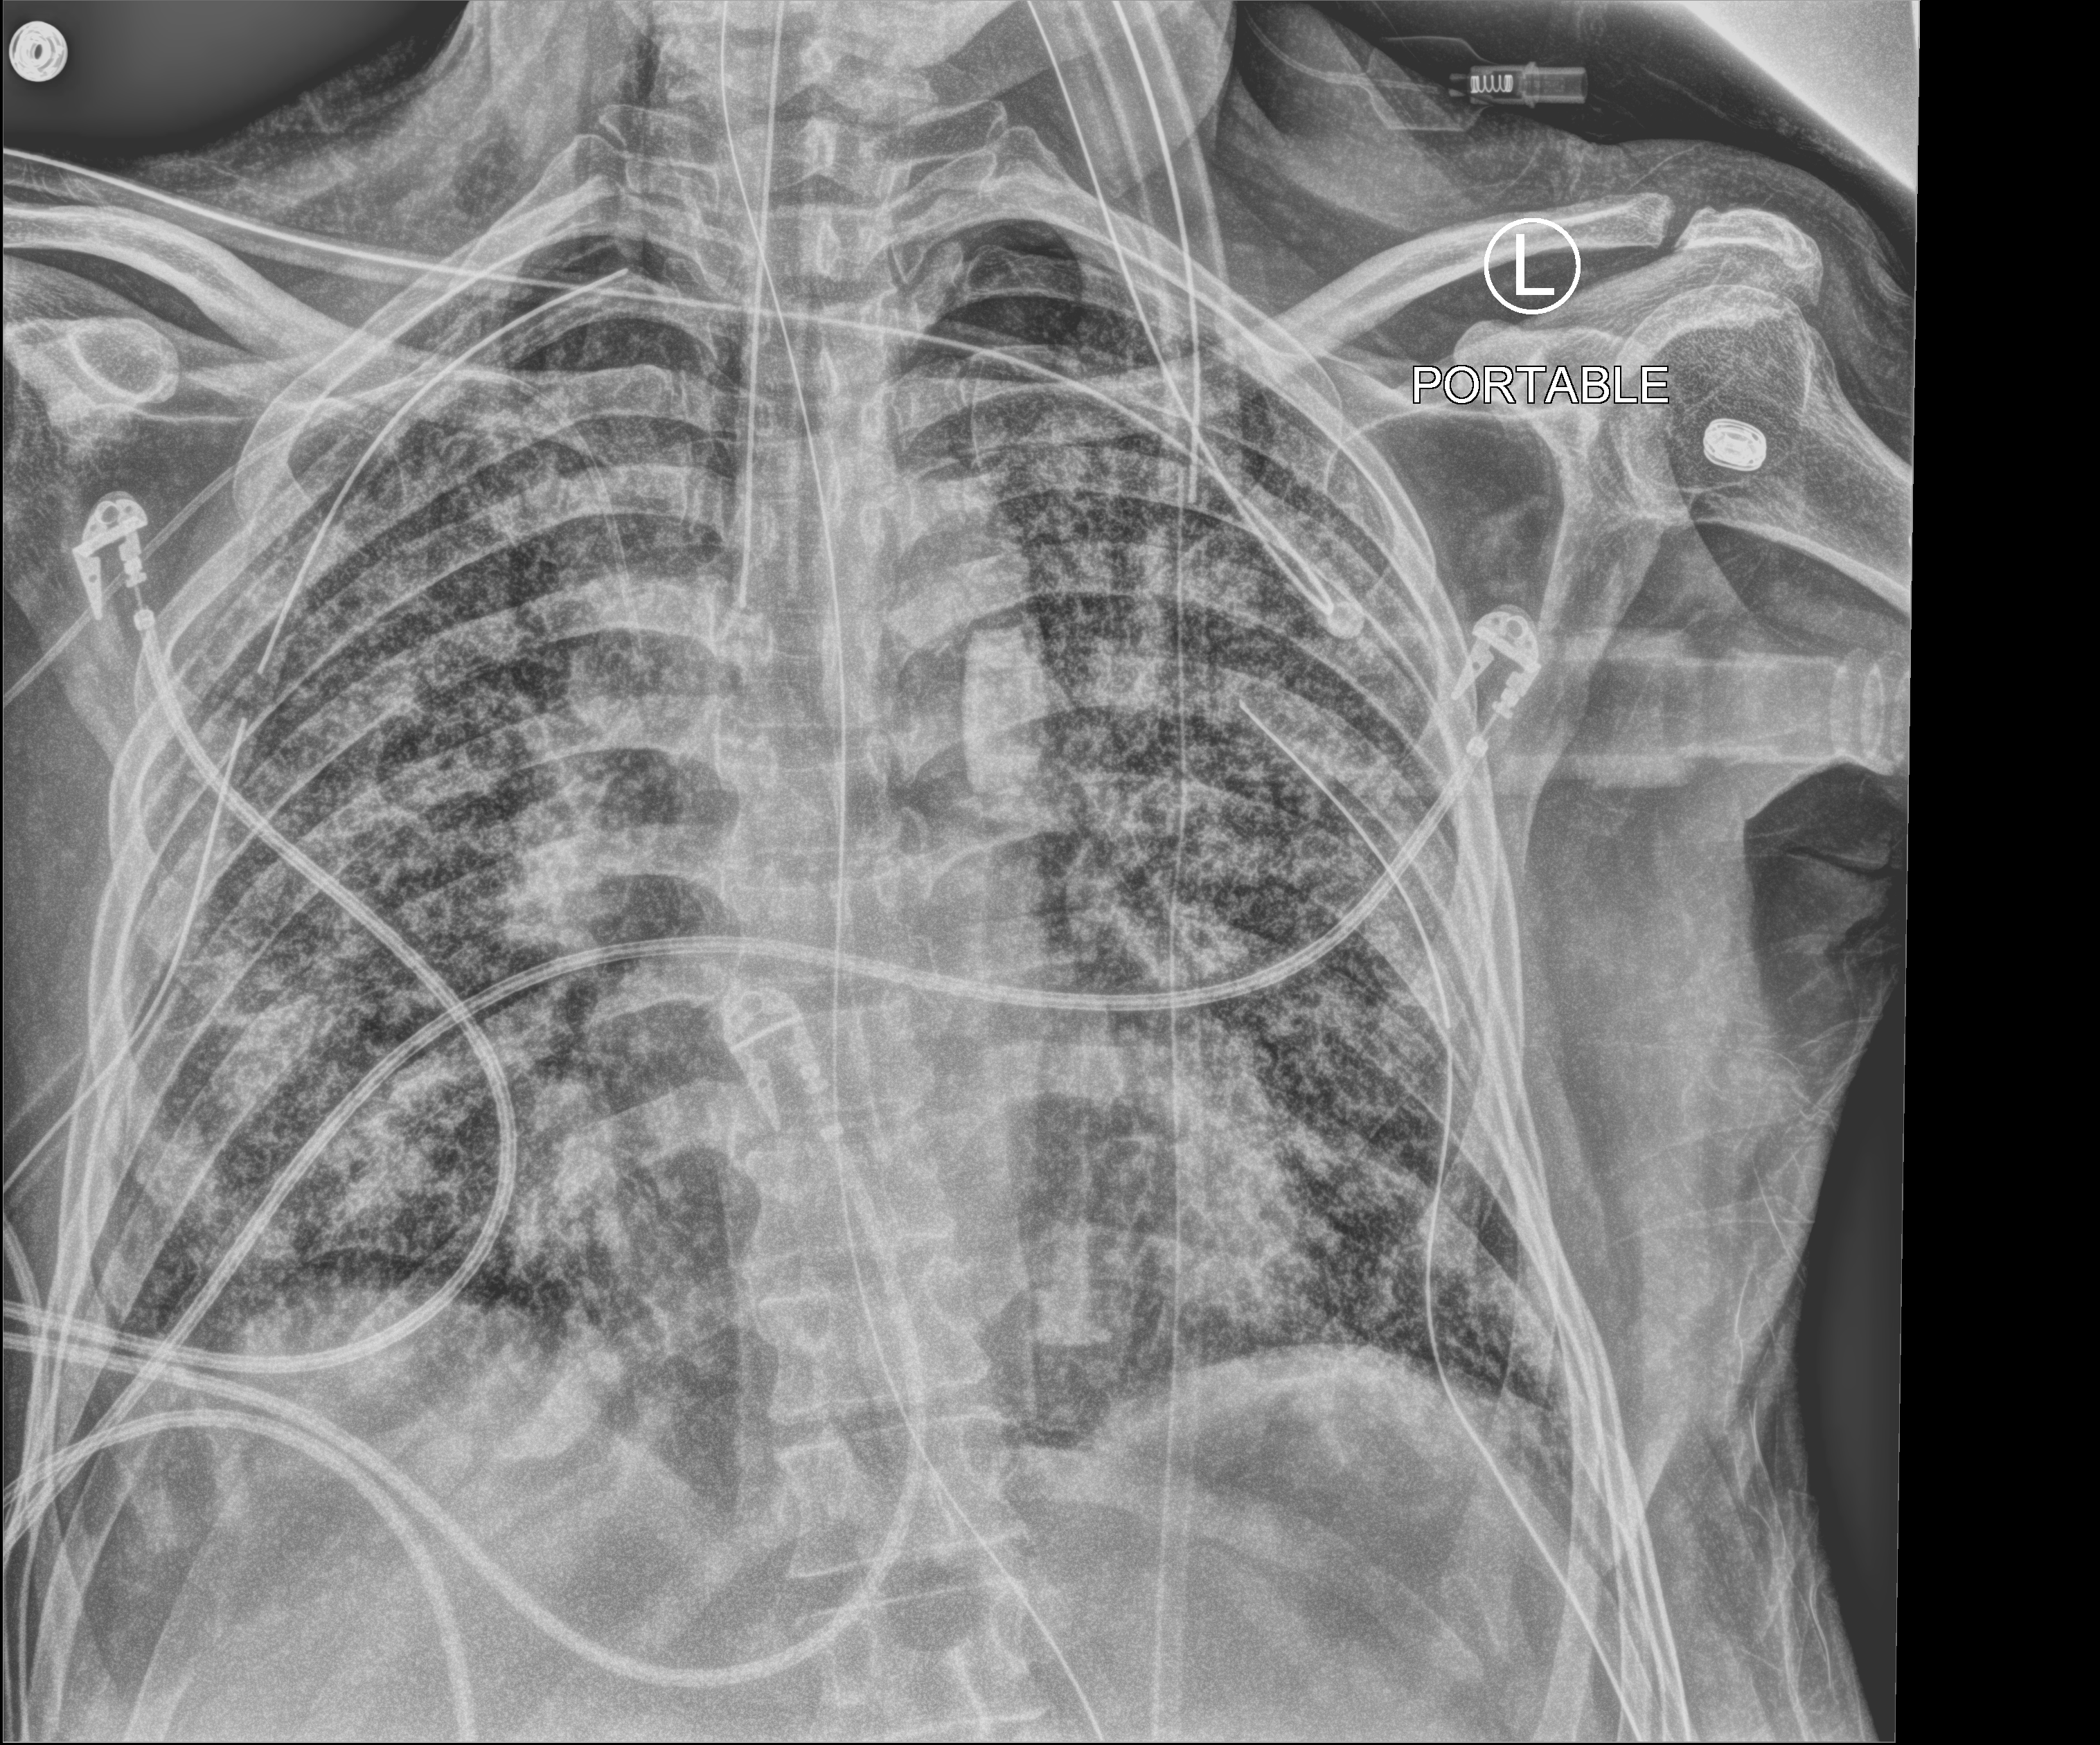
Chest X-ray (portable); anteroposterior (AP) projection. Male patient hospitalised with COVID-19, age 60–74 years.
Admission-level facts for this patient (not findings on this image; timing relative to this image not recorded):
- mechanically ventilated during this hospital stay: yes